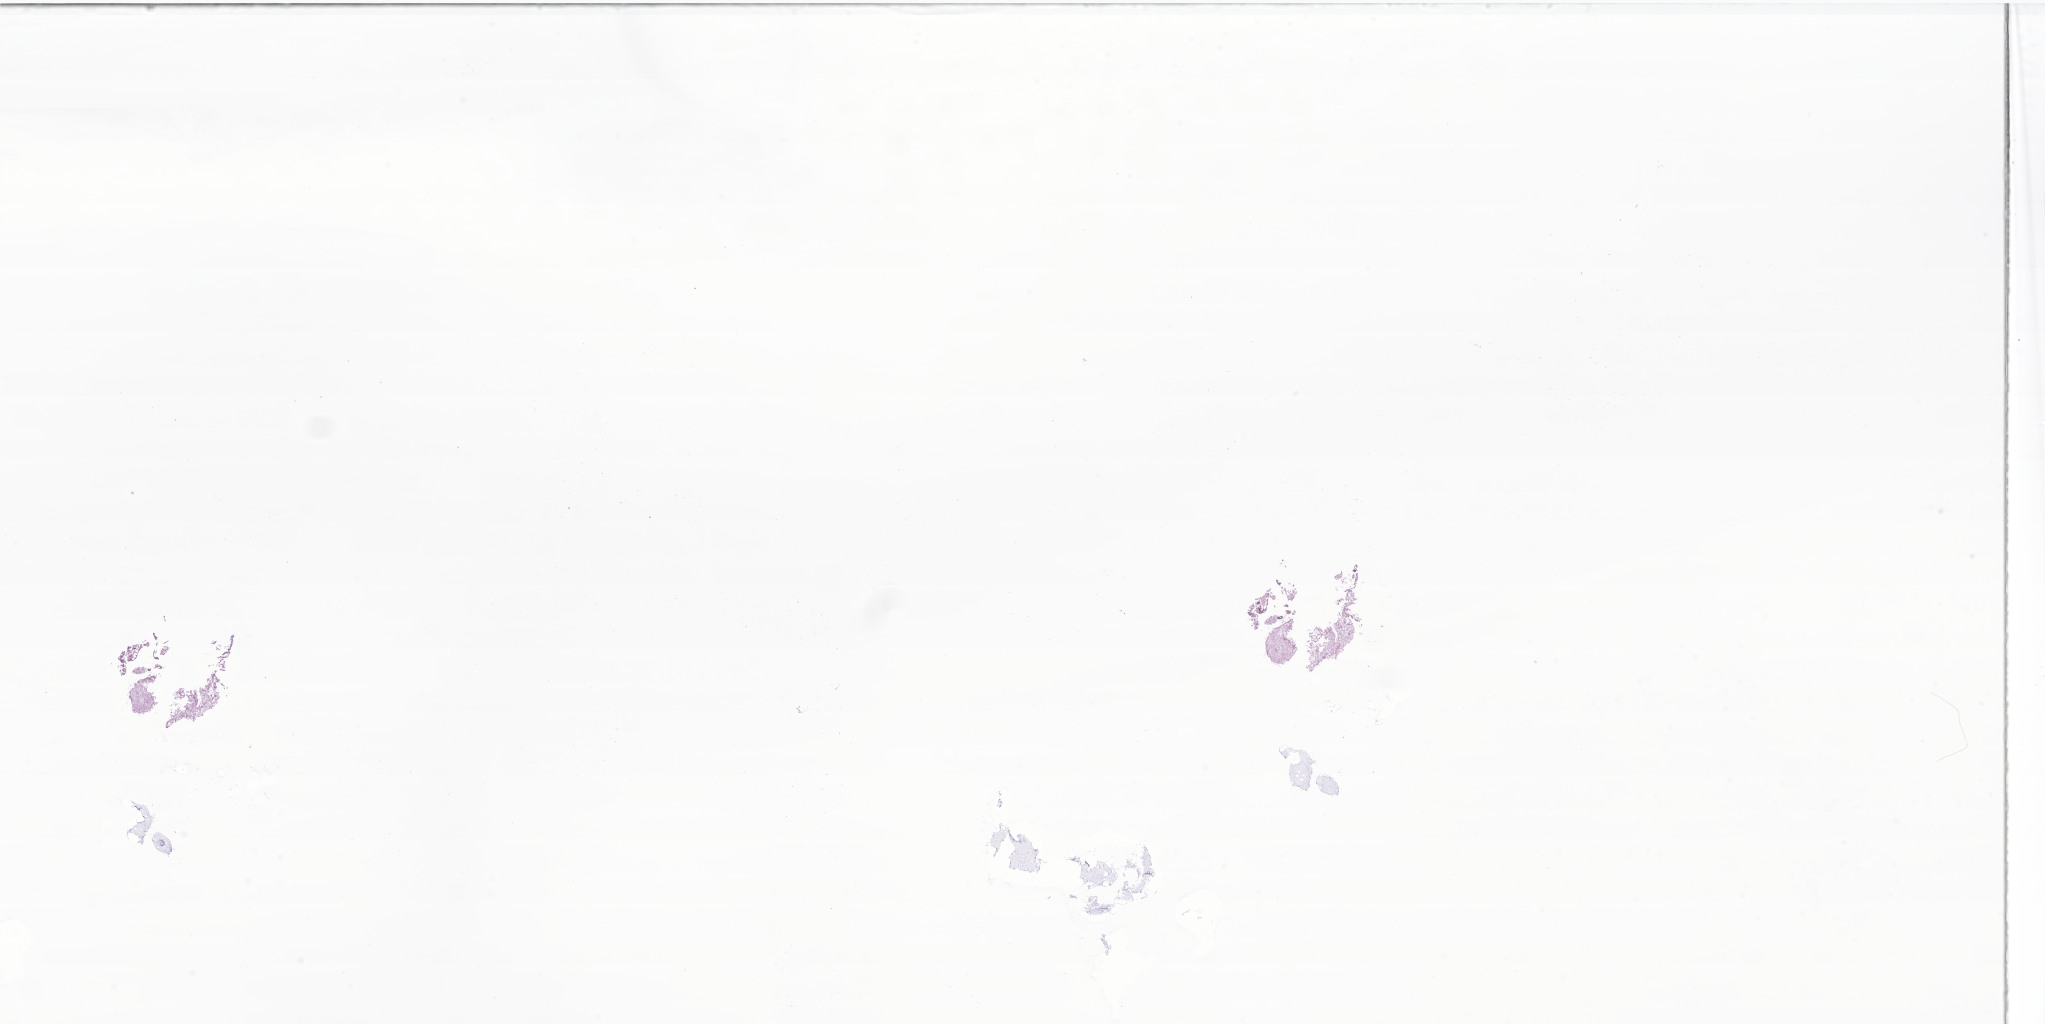
H&E whole-slide image of tumor tissue from the frontal lobe — shown as a low-resolution overview of the whole scanned area (about 34.5 x 17.3 mm); frozen section (OCT-embedded). Patient male; age 56 months (4 years 8 months).
- diagnosis: Neoplasm, uncertain whether benign or malignant